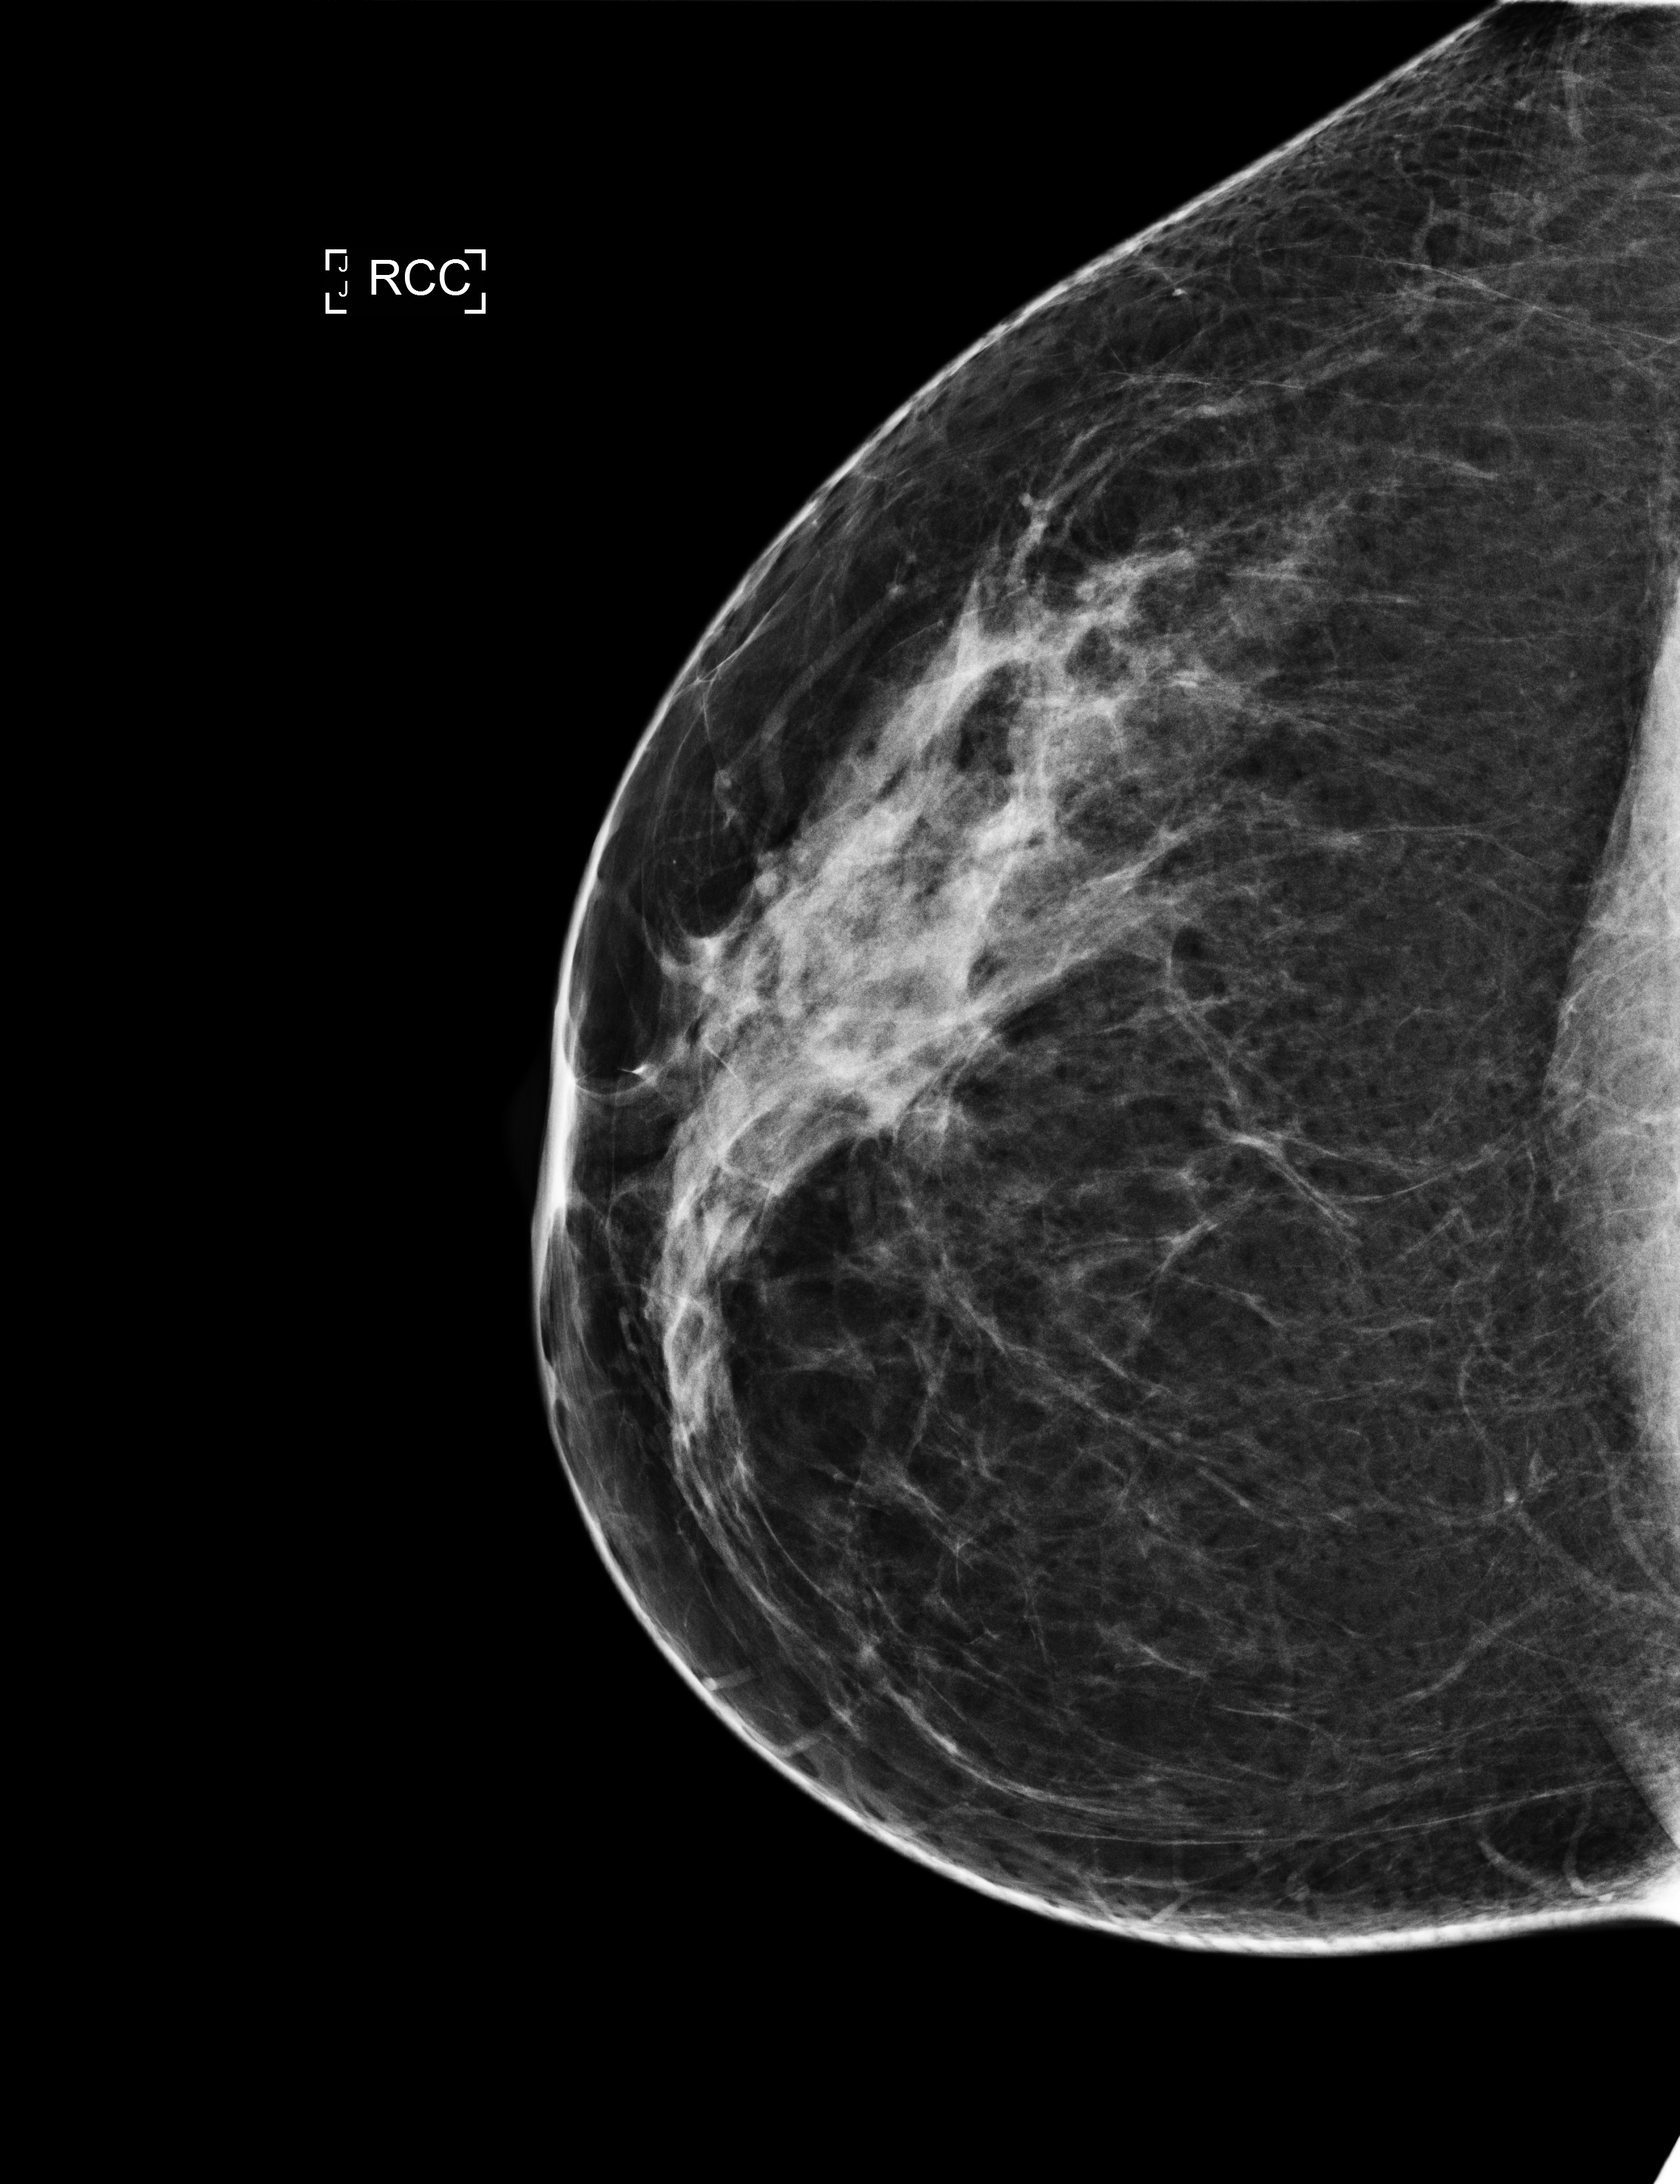
Full-field digital mammogram (FFDM), right breast, CC view, annual screening mammography examination. Female patient, age 41 years.
Breast density at the screening exam (both breasts): scattered fibroglandular densities (BI-RADS density category b).